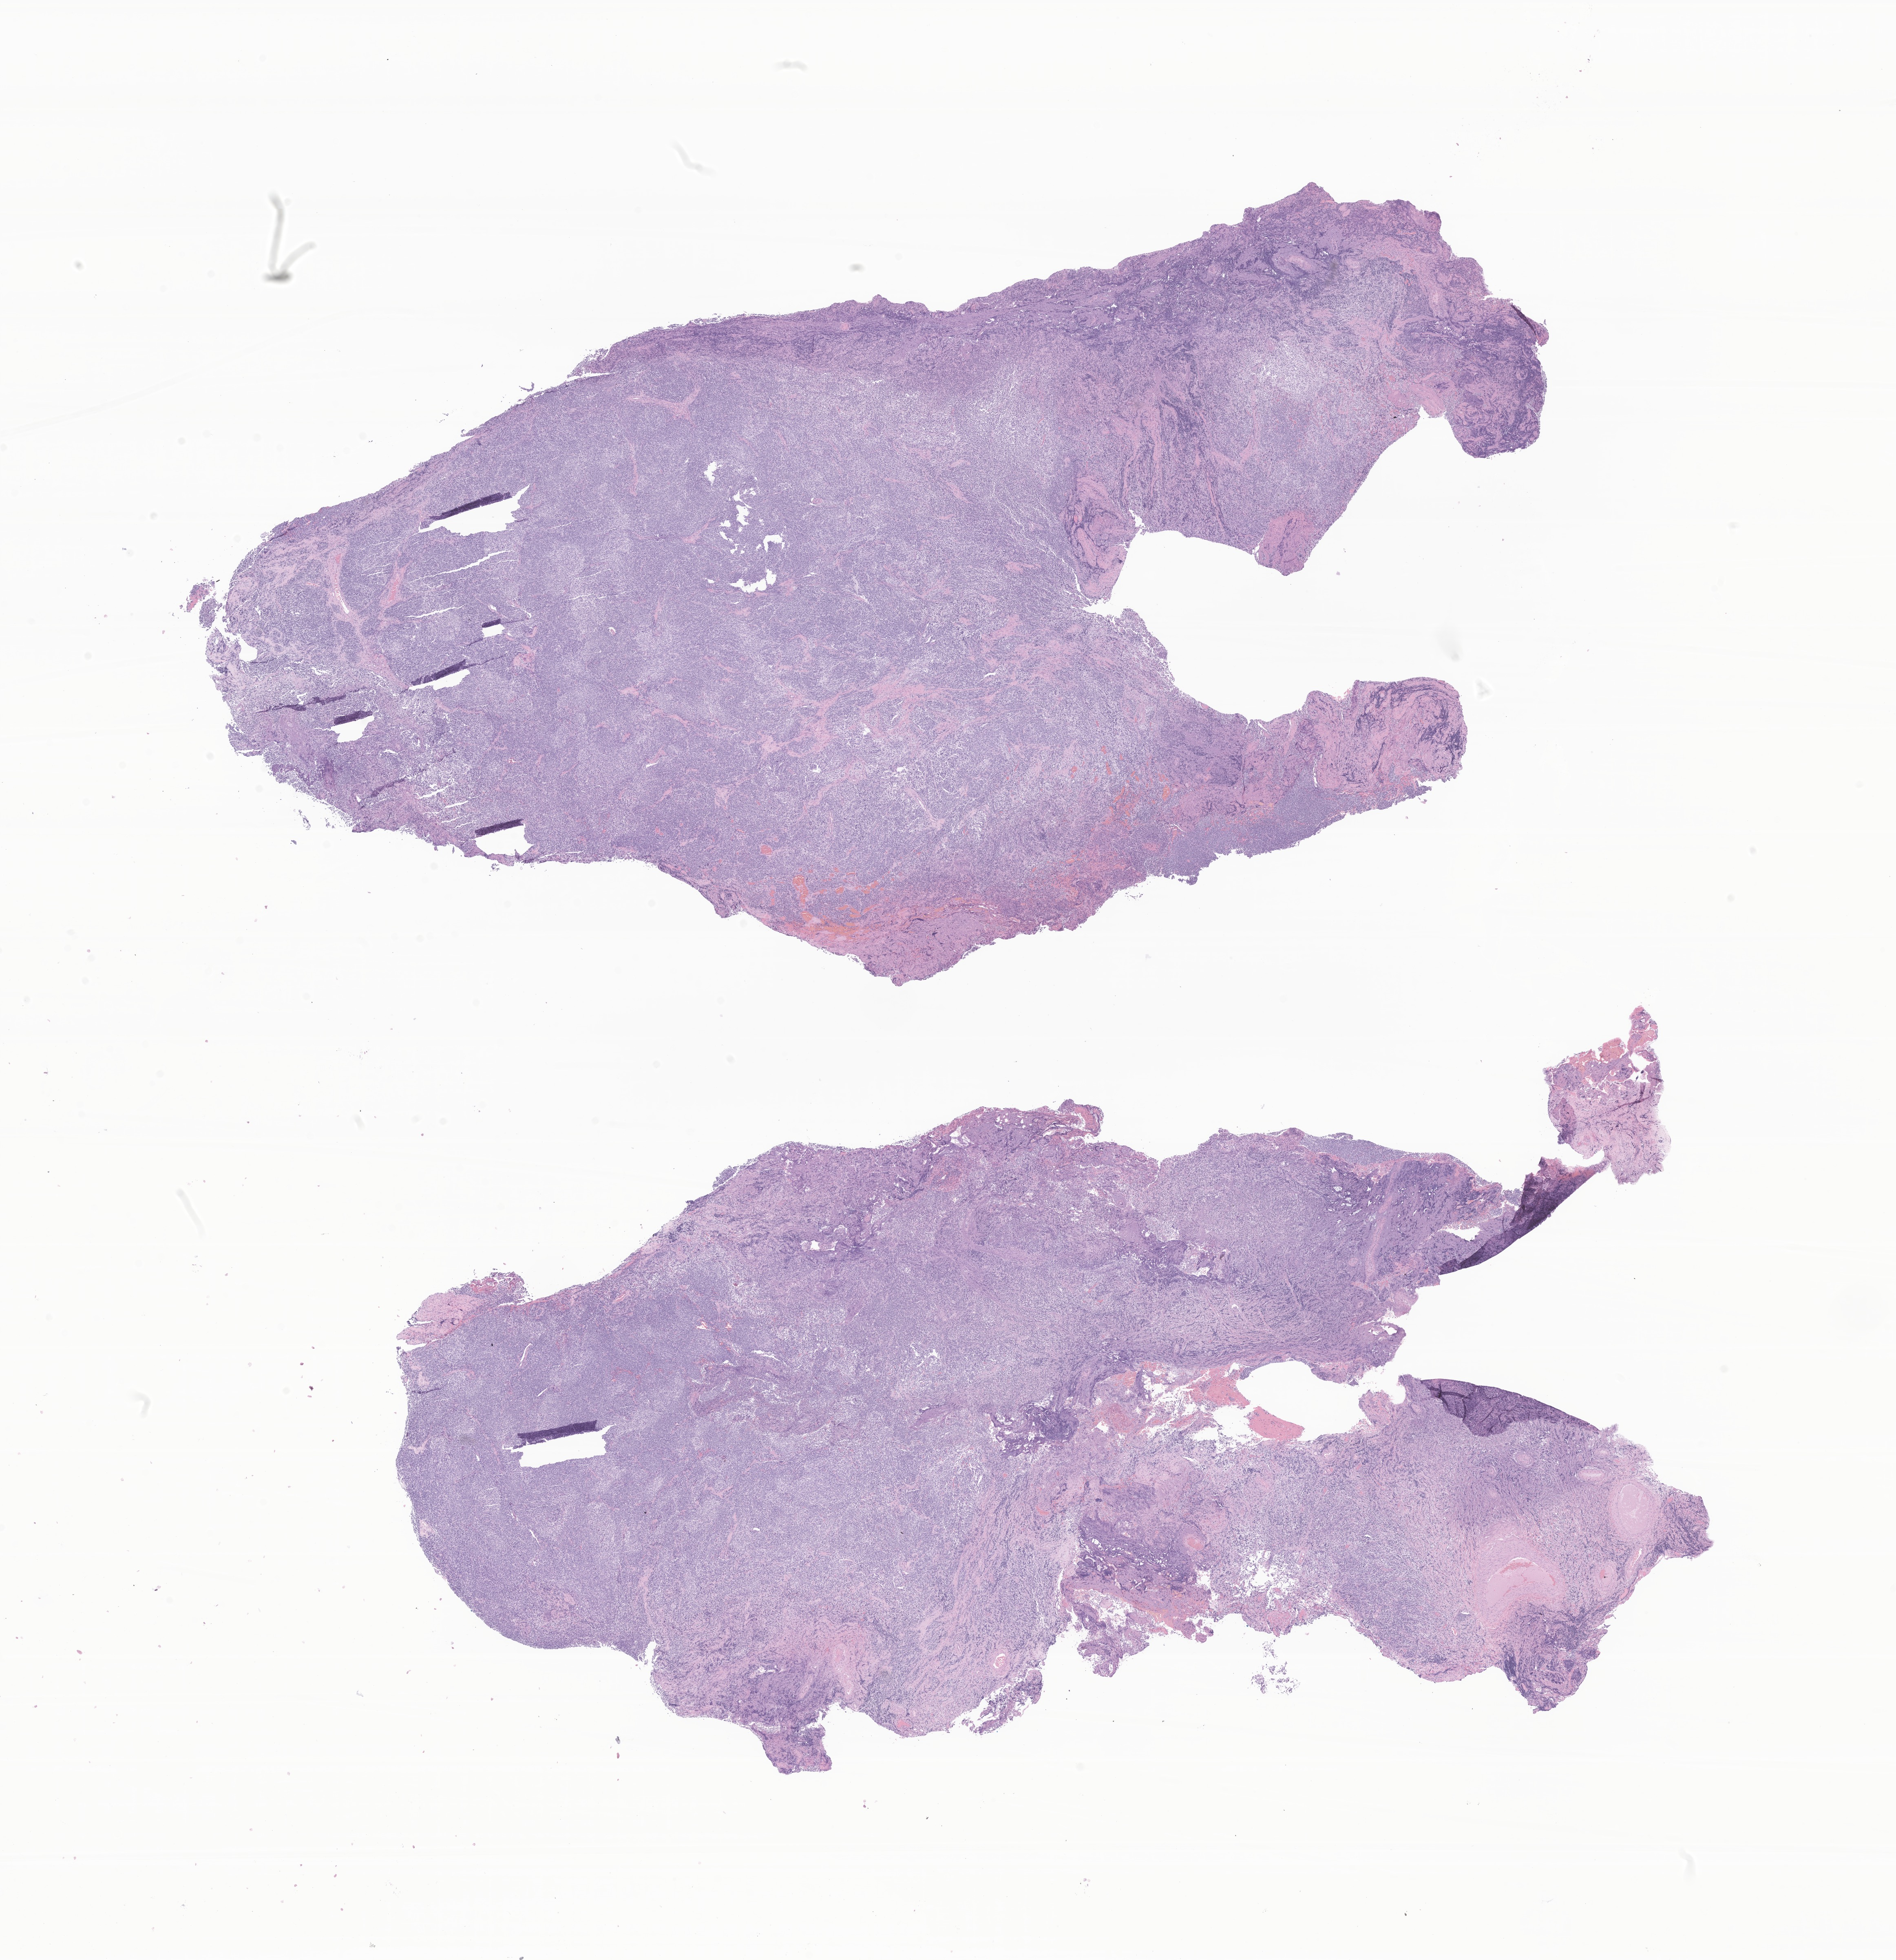
Digitized H&E-stained section of tumor tissue from the brain — shown as a low-resolution overview of the whole scanned area (about 19.6 x 20.3 mm); formalin-fixed paraffin-embedded section. Male patient, age 179 months (14 years 11 months).
Diagnosis (ICD-O-3 morphology term): Medulloblastoma, NOS.